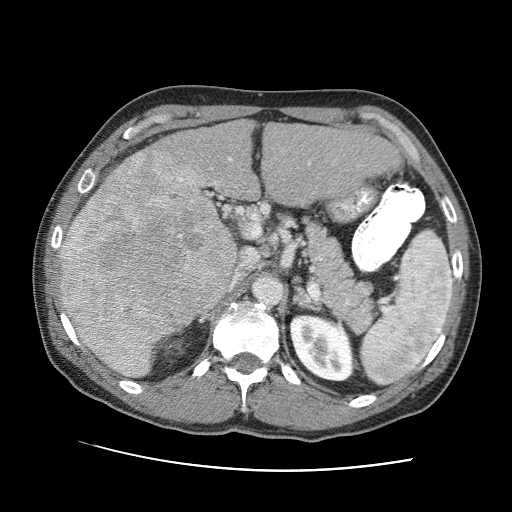
Contrast-enhanced abdominal CT (liver protocol), one axial slice. Position 48 of 95 along the scan axis. 120 kVp. One of 2 acquisitions stored at this slice position. Soft-tissue window (W 400 / L 40 HU). 512 × 512 image matrix, field of view 360 × 360 mm. From the clinical record (not read from this slice): diagnosis: hepatocellular carcinoma (patient treated with transarterial chemoembolisation; whether this scan precedes or follows treatment is not stated here); TNM stage (as recorded): Stage-IVA.
Structures marked on this image (semi-automatic segmentation, software-assisted and operator-edited):
- liver parenchyma outside the tumour (the mass and vessels are separate outlines, so this box may not span the whole liver): bounding box <60,120,398,306> (left, top, right, bottom; pixels)
- mass: <61,146,237,375>
- liver vessels: <62,157,311,253>